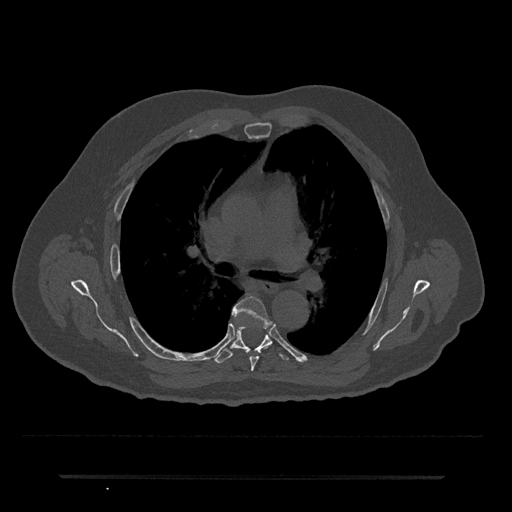
CT including the spine, one axial slice; slice 459 of 797 in the series (ordered by position); 120 kVp; bone window (W 1800 / L 400 HU); 0.5 mm slice thickness; 512 × 512 image matrix, field of view 437 × 437 mm. Patient: male, 69 years. Case-level facts recorded for this patient, not image findings: primary cancer: prostate.
Outlined on this slice (semi-automatically segmented with operator editing):
- T5 vertebra: bounding box <232,296,273,371> (left, top, right, bottom; pixels)
- T6 vertebra: <215,320,289,364>